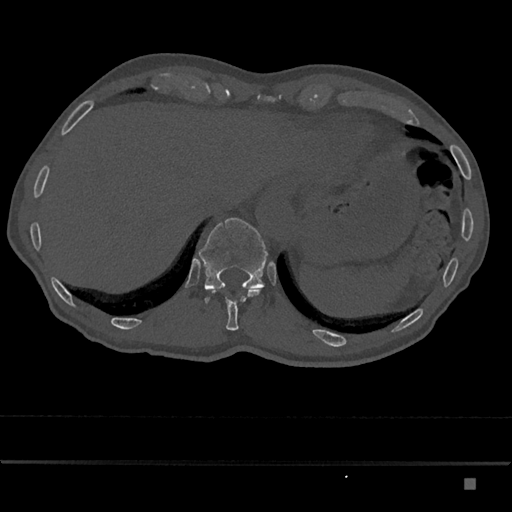
CT including the spine, one axial slice. Slice 643 of 797 in the series (ordered by position). Reconstruction kernel Br40s/3. 120 kVp. Bone window (W 1800 / L 400 HU). 0.5 mm slice thickness. 512 × 512 image matrix, field of view 390 × 390 mm. Patient: male, 72 years. From the clinical record (not read from this slice): primary cancer: prostate.
Structures marked on this image (semi-automatically segmented with operator editing):
- T11 vertebra: bounding box [x1, y1, x2, y2] px = [212, 288, 260, 331]
- T12 vertebra: [199, 218, 268, 304]